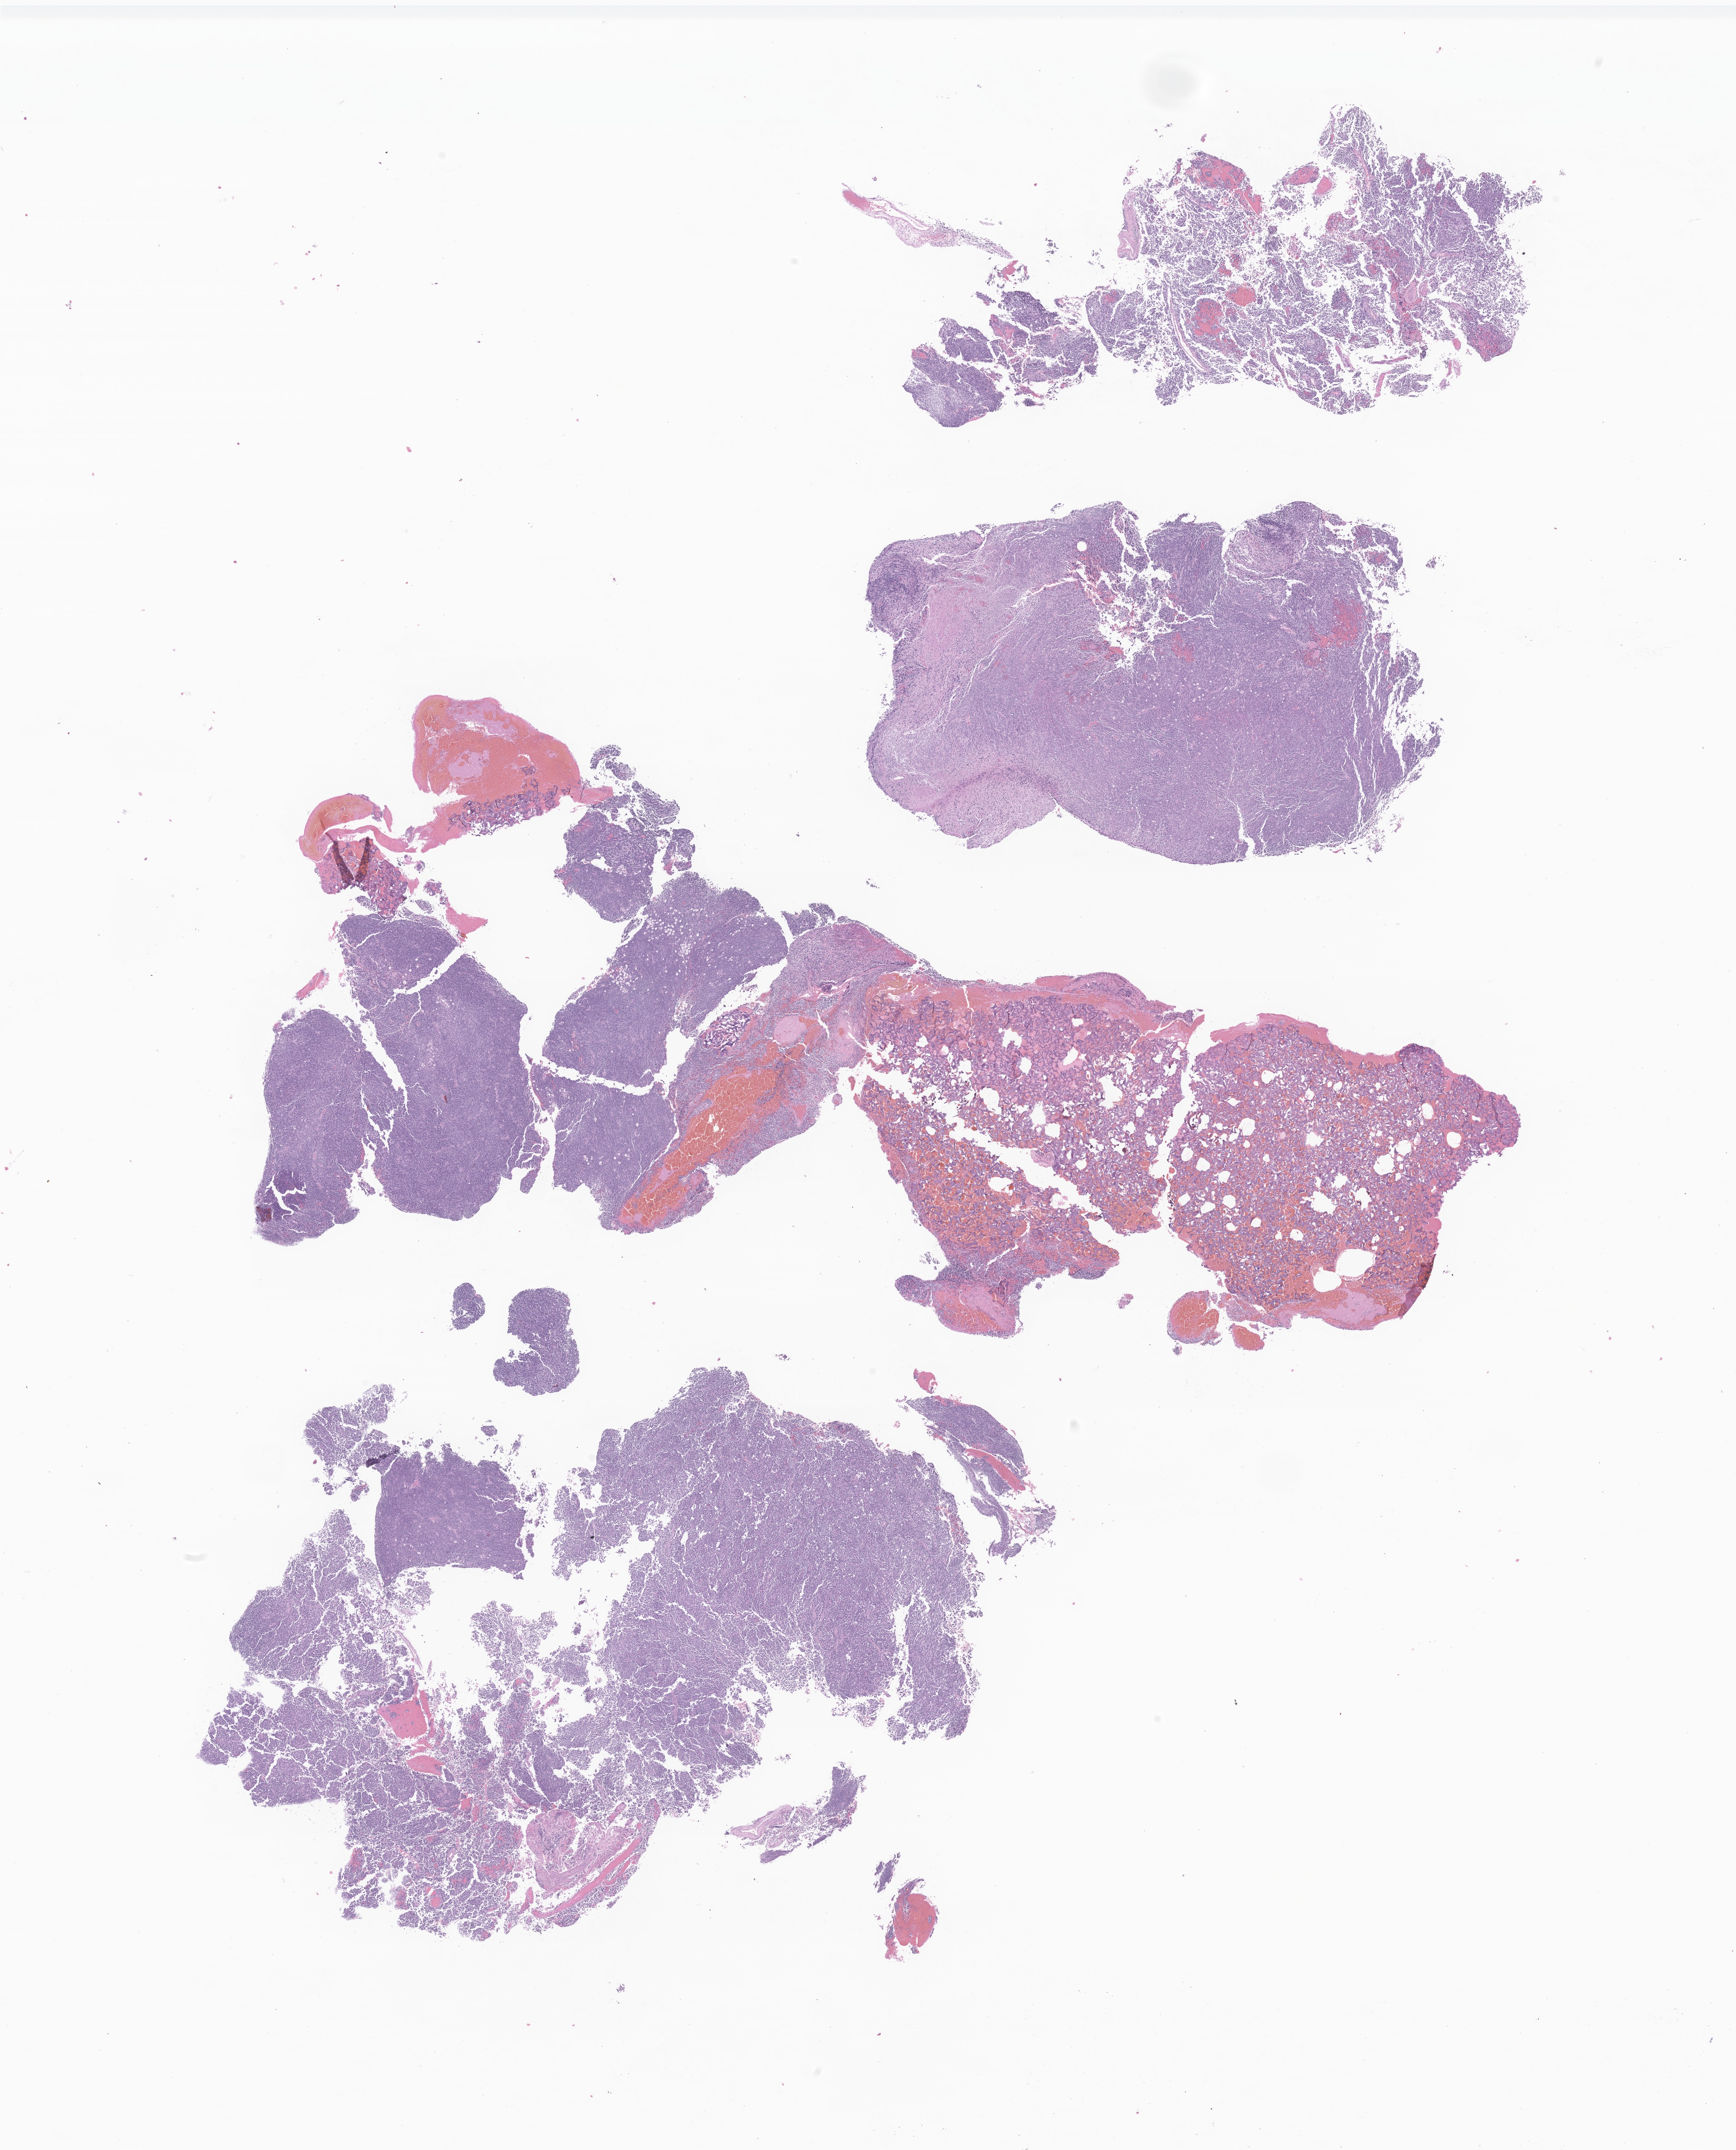
Digitized haematoxylin and eosin-stained section of tumor tissue from the brain, shown as a low-resolution overview of the whole scanned area (about 17.3 x 21.5 mm). Formalin-fixed paraffin-embedded section. Female patient, age 46 months (3 years 10 months).
Diagnosis: Medulloblastoma, NOS.